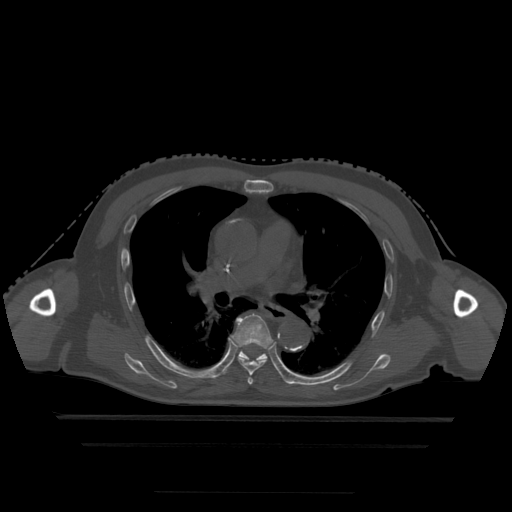
CT including the spine, one axial slice; position 312 of 522 along the scan axis; bone window (W 1800 / L 400 HU); 1.25 mm slice thickness; 512 × 512 image matrix, field of view 436 × 436 mm. Patient age 68 years. Case-level facts recorded for this patient, not image findings: primary cancer: urothelial.
Structures marked on this image (semi-automatically segmented with operator editing):
- T5 vertebra: bounding box (x1, y1, x2, y2) in pixels: (248, 376, 254, 385)
- T6 vertebra: (231, 313, 273, 376)
- T7 vertebra: (225, 343, 284, 379)